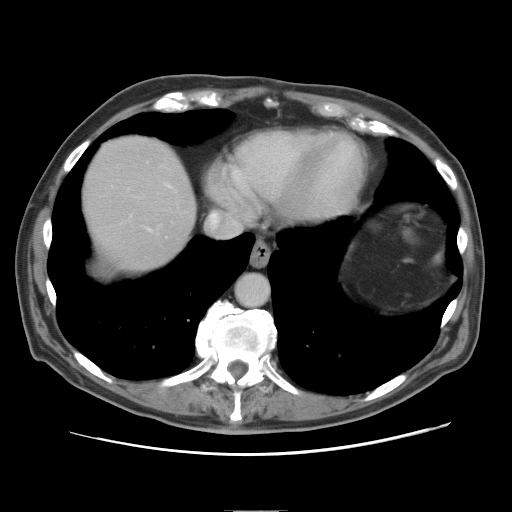
Contrast-enhanced abdominal CT, one axial slice; slice 73 of 89 in the series (ordered by position); soft-tissue window (W 400 / L 40 HU); 5 mm slice thickness; 512 × 512 image matrix. Male patient, age 69 years. From the clinical record (not read from this slice): diagnosis: colorectal cancer liver metastases, imaged before liver resection; multiple liver metastases: no; largest metastasis: 8.5 cm; chemotherapy before resection: no.
Annotated regions visible in this slice (outlined manually by an expert reader):
- hepatic veins: box from (x=148, y=227) to (x=152, y=231) px
- liver: (x=83, y=137)–(x=195, y=277)
- planned liver remnant (the part of the liver to remain after resection): (x=83, y=136)–(x=196, y=275)
- portal vein (with intrahepatic branches): (x=130, y=215)–(x=132, y=217)